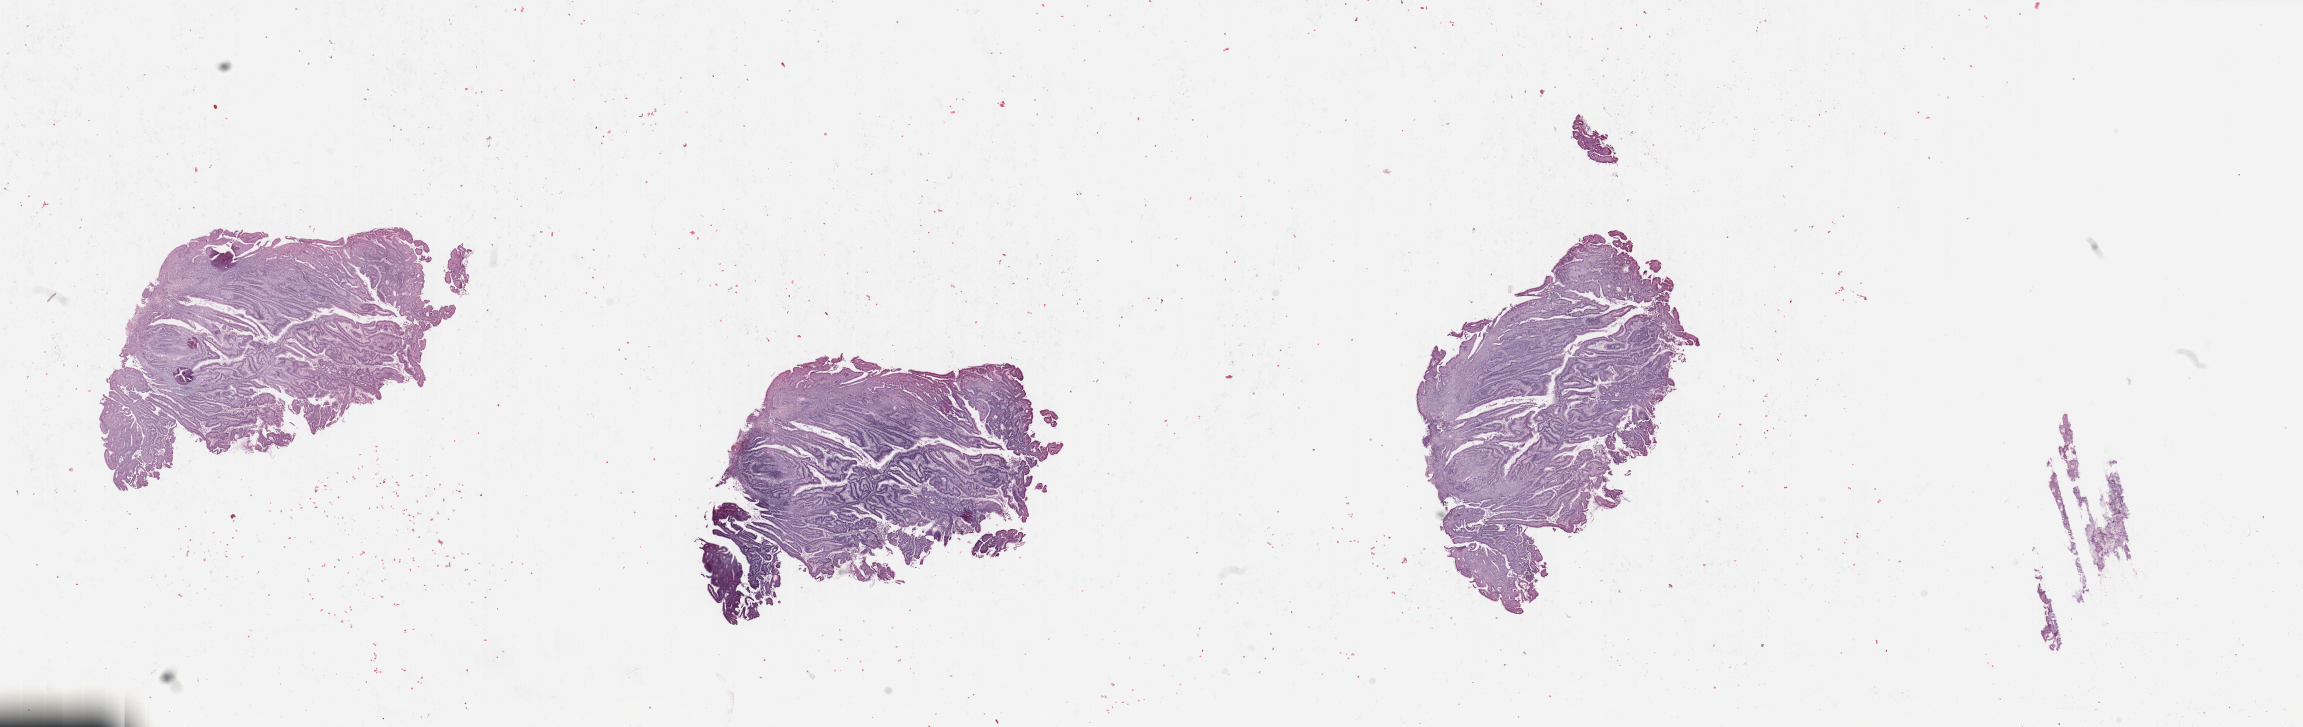
Digitized H&E-stained tissue section (whole slide) — shown as a low-resolution overview of the whole scanned area (about 36.4 x 11.5 mm, from a 20x scan), tumour tissue sample, sampled site: uterus. Female, 53 y/o. Pathologist review of this section (percent, as recorded): tumour nuclei 80%, necrosis 2%.
Histologic diagnosis: Endometrioid adenocarcinoma, NOS.